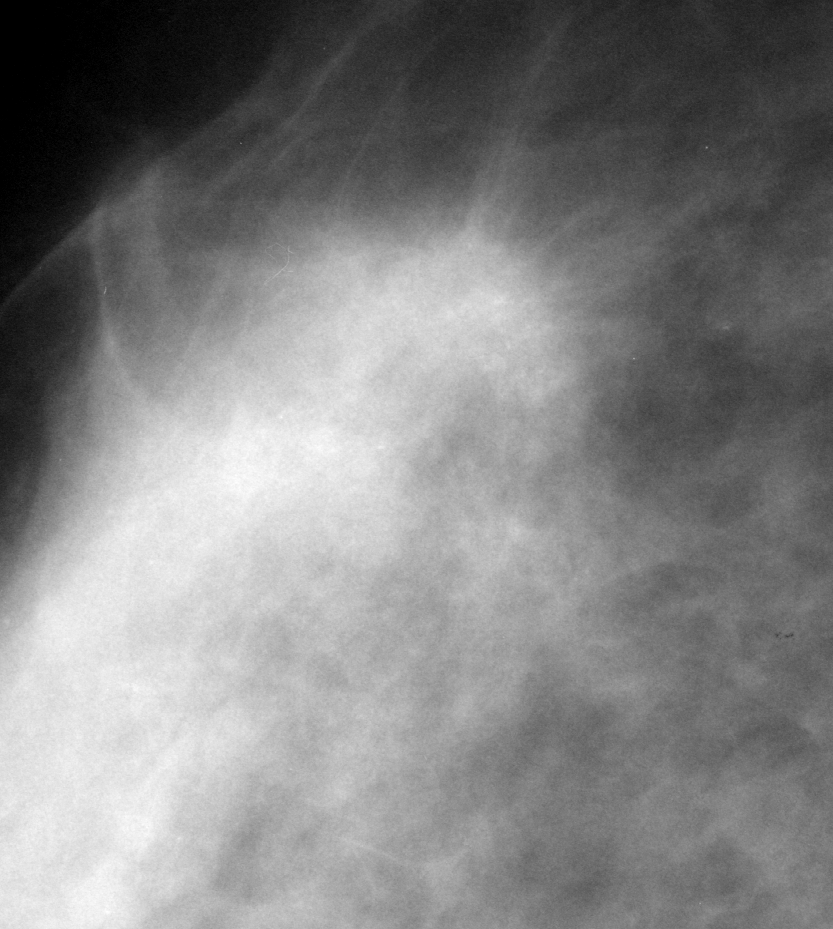
Crop from a digitized film mammogram around one marked abnormality, right breast, MLO view.
- Calcifications, morphology amorphous, distribution clustered; BI-RADS assessment category 5; subtlety rating 5 on a 1 (subtle) to 5 (obvious) scale; pathology result (as recorded, not read from the image): malignant.